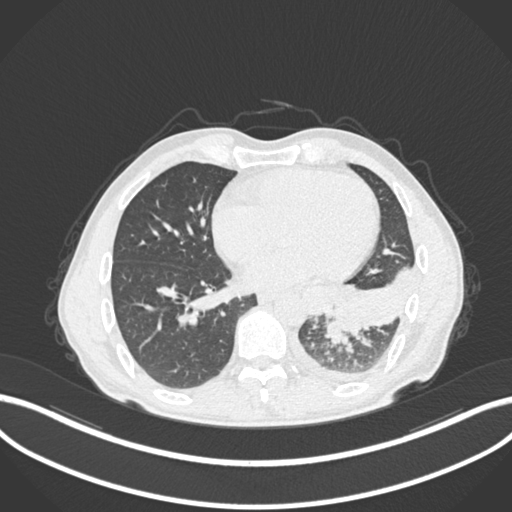
Chest CT, one axial slice; slice 91 of 222 in the series (ordered by position); reconstruction kernel B30f; lung window (W 1500 / L -600 HU); 1 mm slice thickness; 512 × 512 image matrix. Male patient, age 47 years. From the clinical record (not read from this slice): clinical TNM (as recorded): T3 N1 M1c.
Annotated regions visible in this slice (rectangle marked by the reading radiologist):
- lung tumour (recorded histology: small cell carcinoma): bounding box <323,317,350,348> (left, top, right, bottom; pixels)